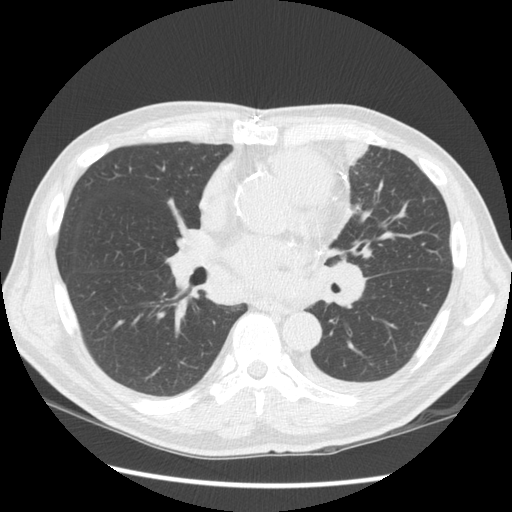
Low-dose screening chest CT, one axial slice. Slice 74 of 136 in the series (ordered by position). Reconstruction kernel STANDARD. Lung window (W 1500 / L -600 HU). 2.5 mm slice thickness. 512 × 512 image matrix, field of view 360 × 360 mm.
Outlined on this slice (manually delineated by an expert):
- lesion 1 (tumor, upper lobe of left lung): box from (x=329, y=139) to (x=367, y=168) px